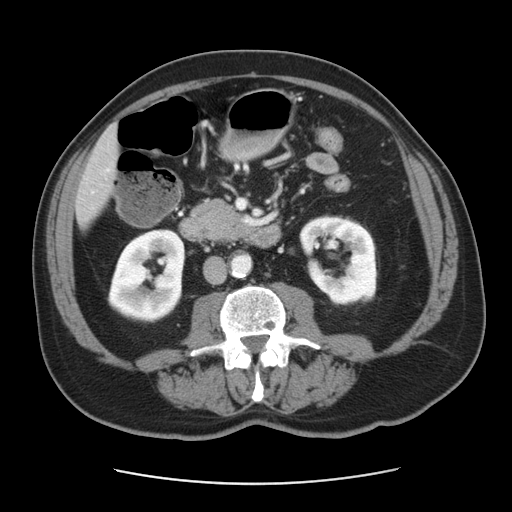
Contrast-enhanced abdominal CT, one axial slice. Position 13 of 42 along the scan axis. Soft-tissue window (W 400 / L 40 HU). 5 mm slice thickness. 512 × 512 image matrix. Male patient, age 73 years. From the clinical record (not read from this slice): diagnosis: colorectal cancer liver metastases, imaged before liver resection; multiple liver metastases: yes; largest metastasis: 0.5 cm.
Structures marked on this image (outlined manually by an expert reader):
- liver: bounding box <77,130,117,225> (left, top, right, bottom; pixels)
- planned liver remnant (the part of the liver to remain after resection): <108,130,115,139>